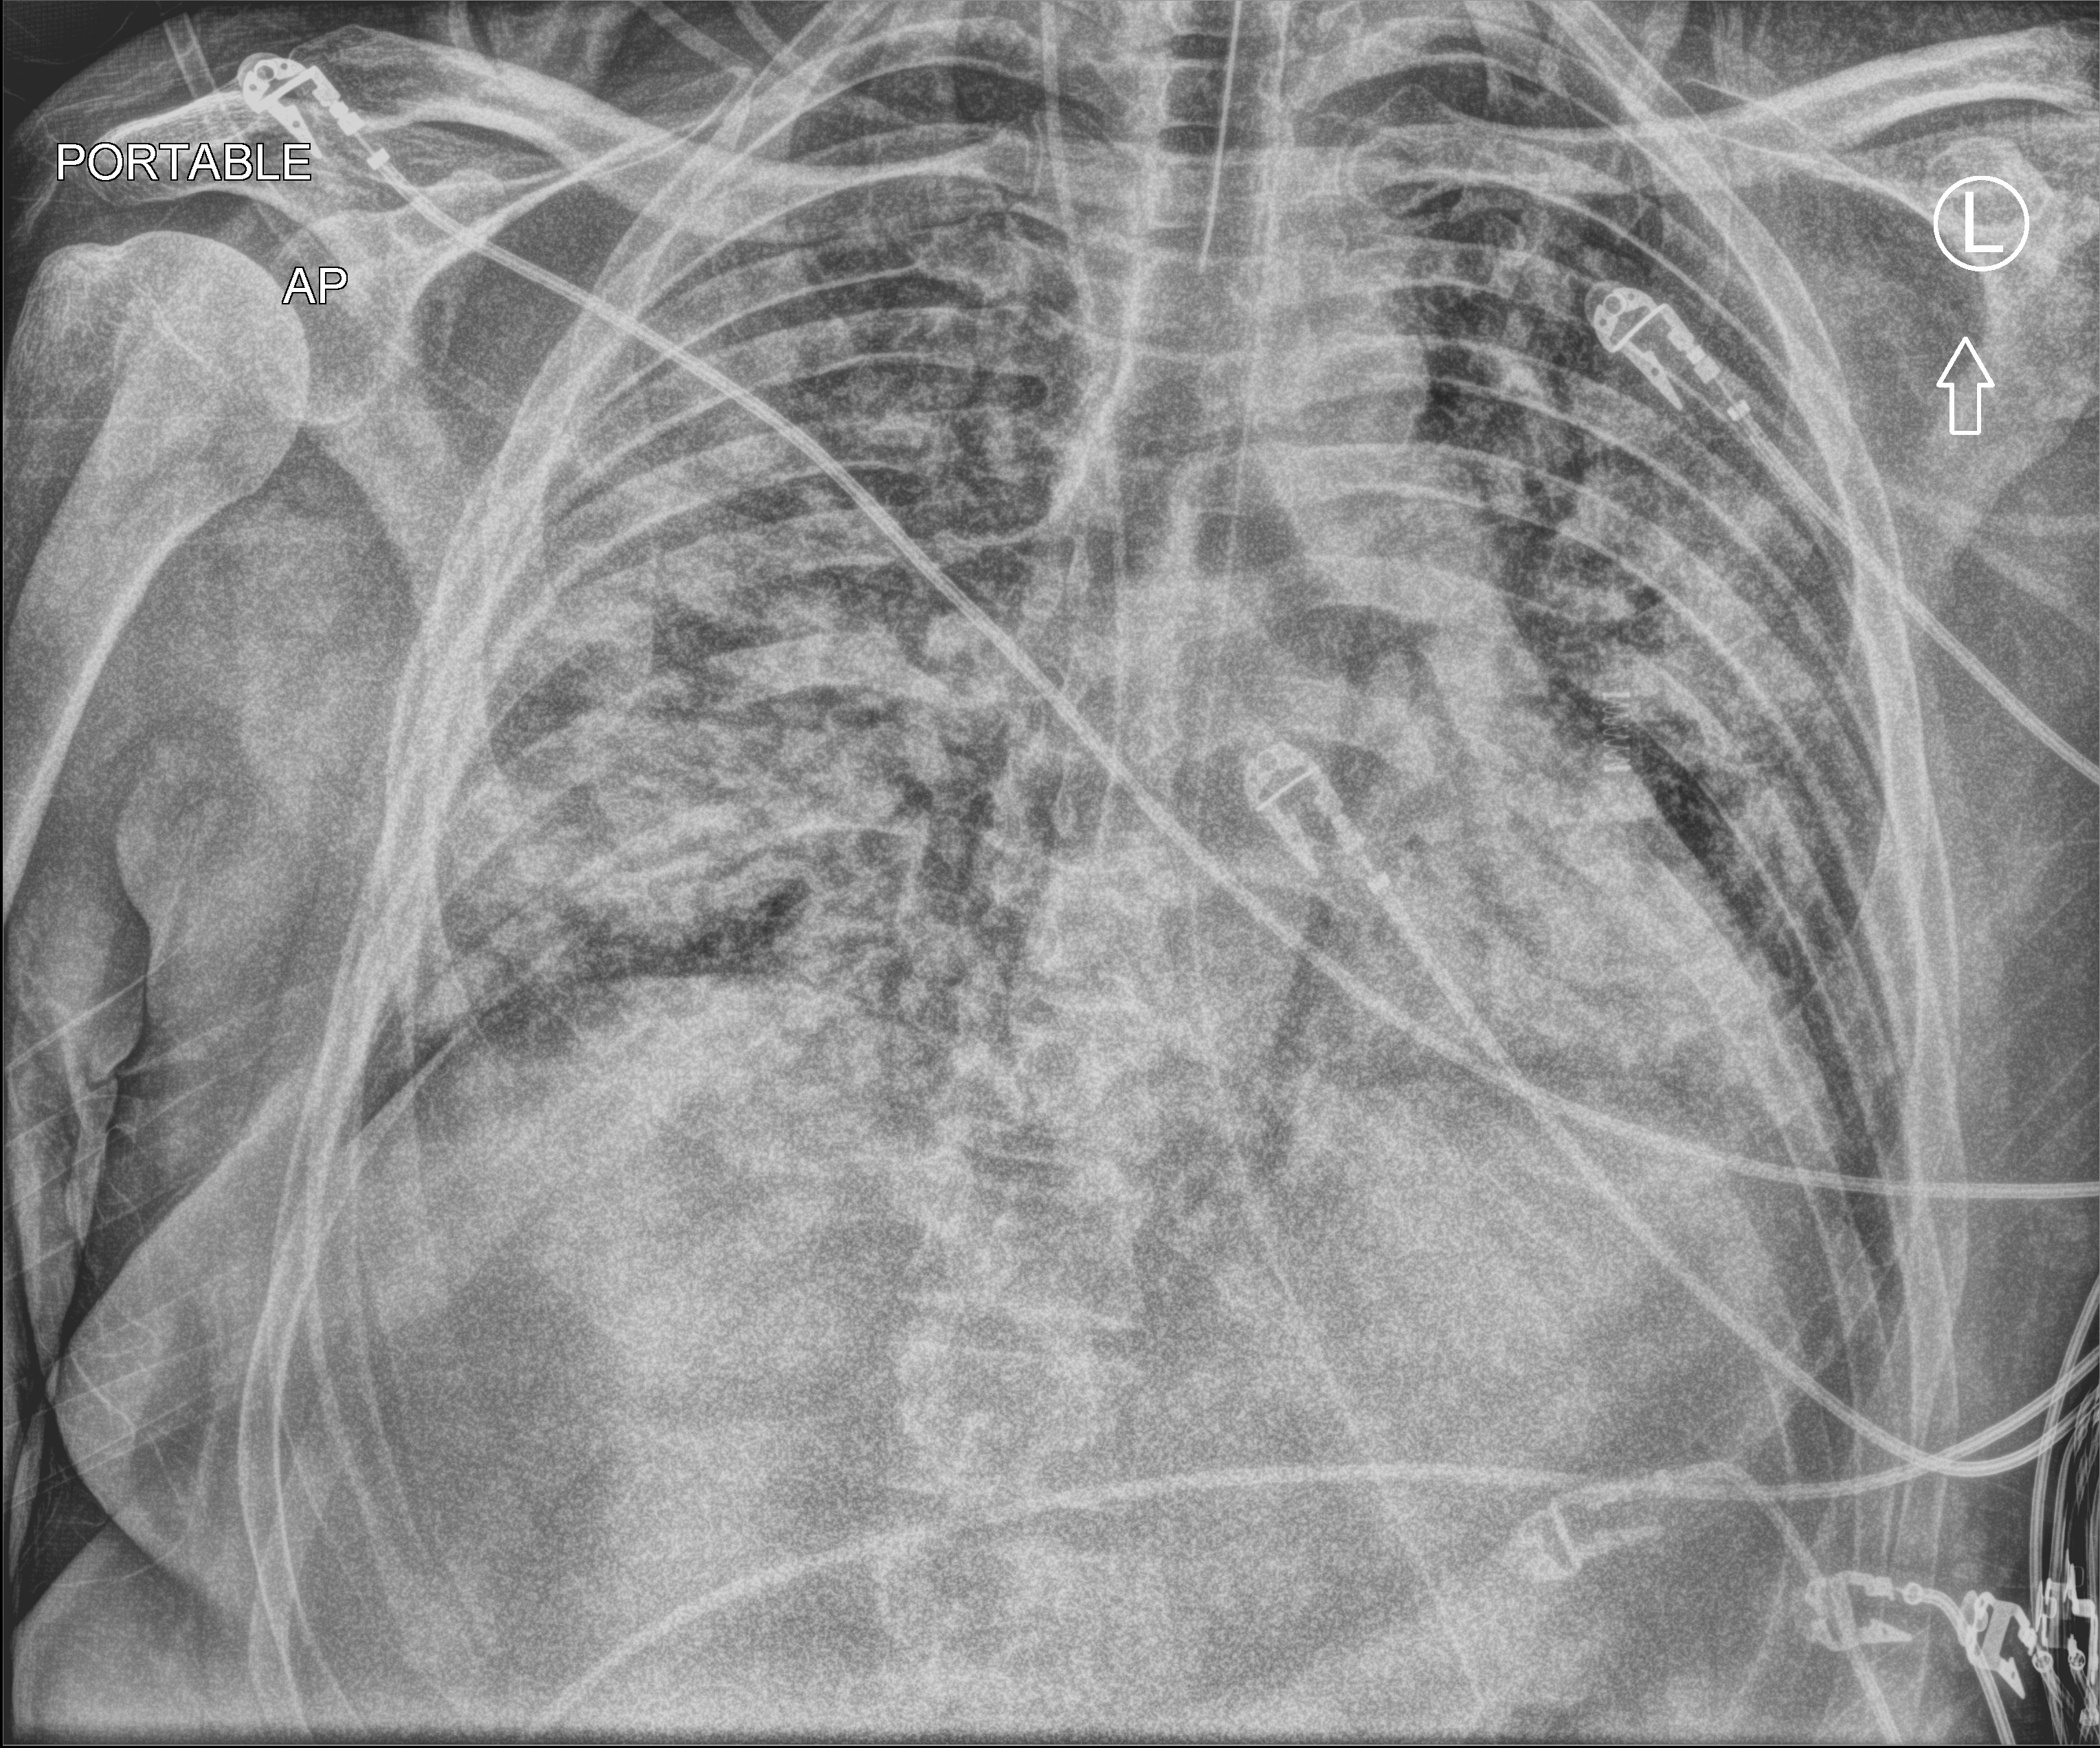
Chest X-ray (portable); anteroposterior (AP) projection. Patient hospitalised with COVID-19; male, aged 18–59 years.
Admission-level facts for this patient (not findings on this image; timing relative to this image not recorded): admitted to intensive care during this hospital stay: yes; length of hospital stay: 75 days; hypertension (admission record): no.